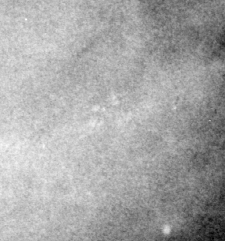
Crop from a digitized film mammogram around one marked abnormality, right breast, MLO view.
Finding: calcifications, morphology pleomorphic, distribution clustered; BI-RADS assessment category 4; subtlety rating 3 on a 1 (subtle) to 5 (obvious) scale; pathology (as recorded): benign.